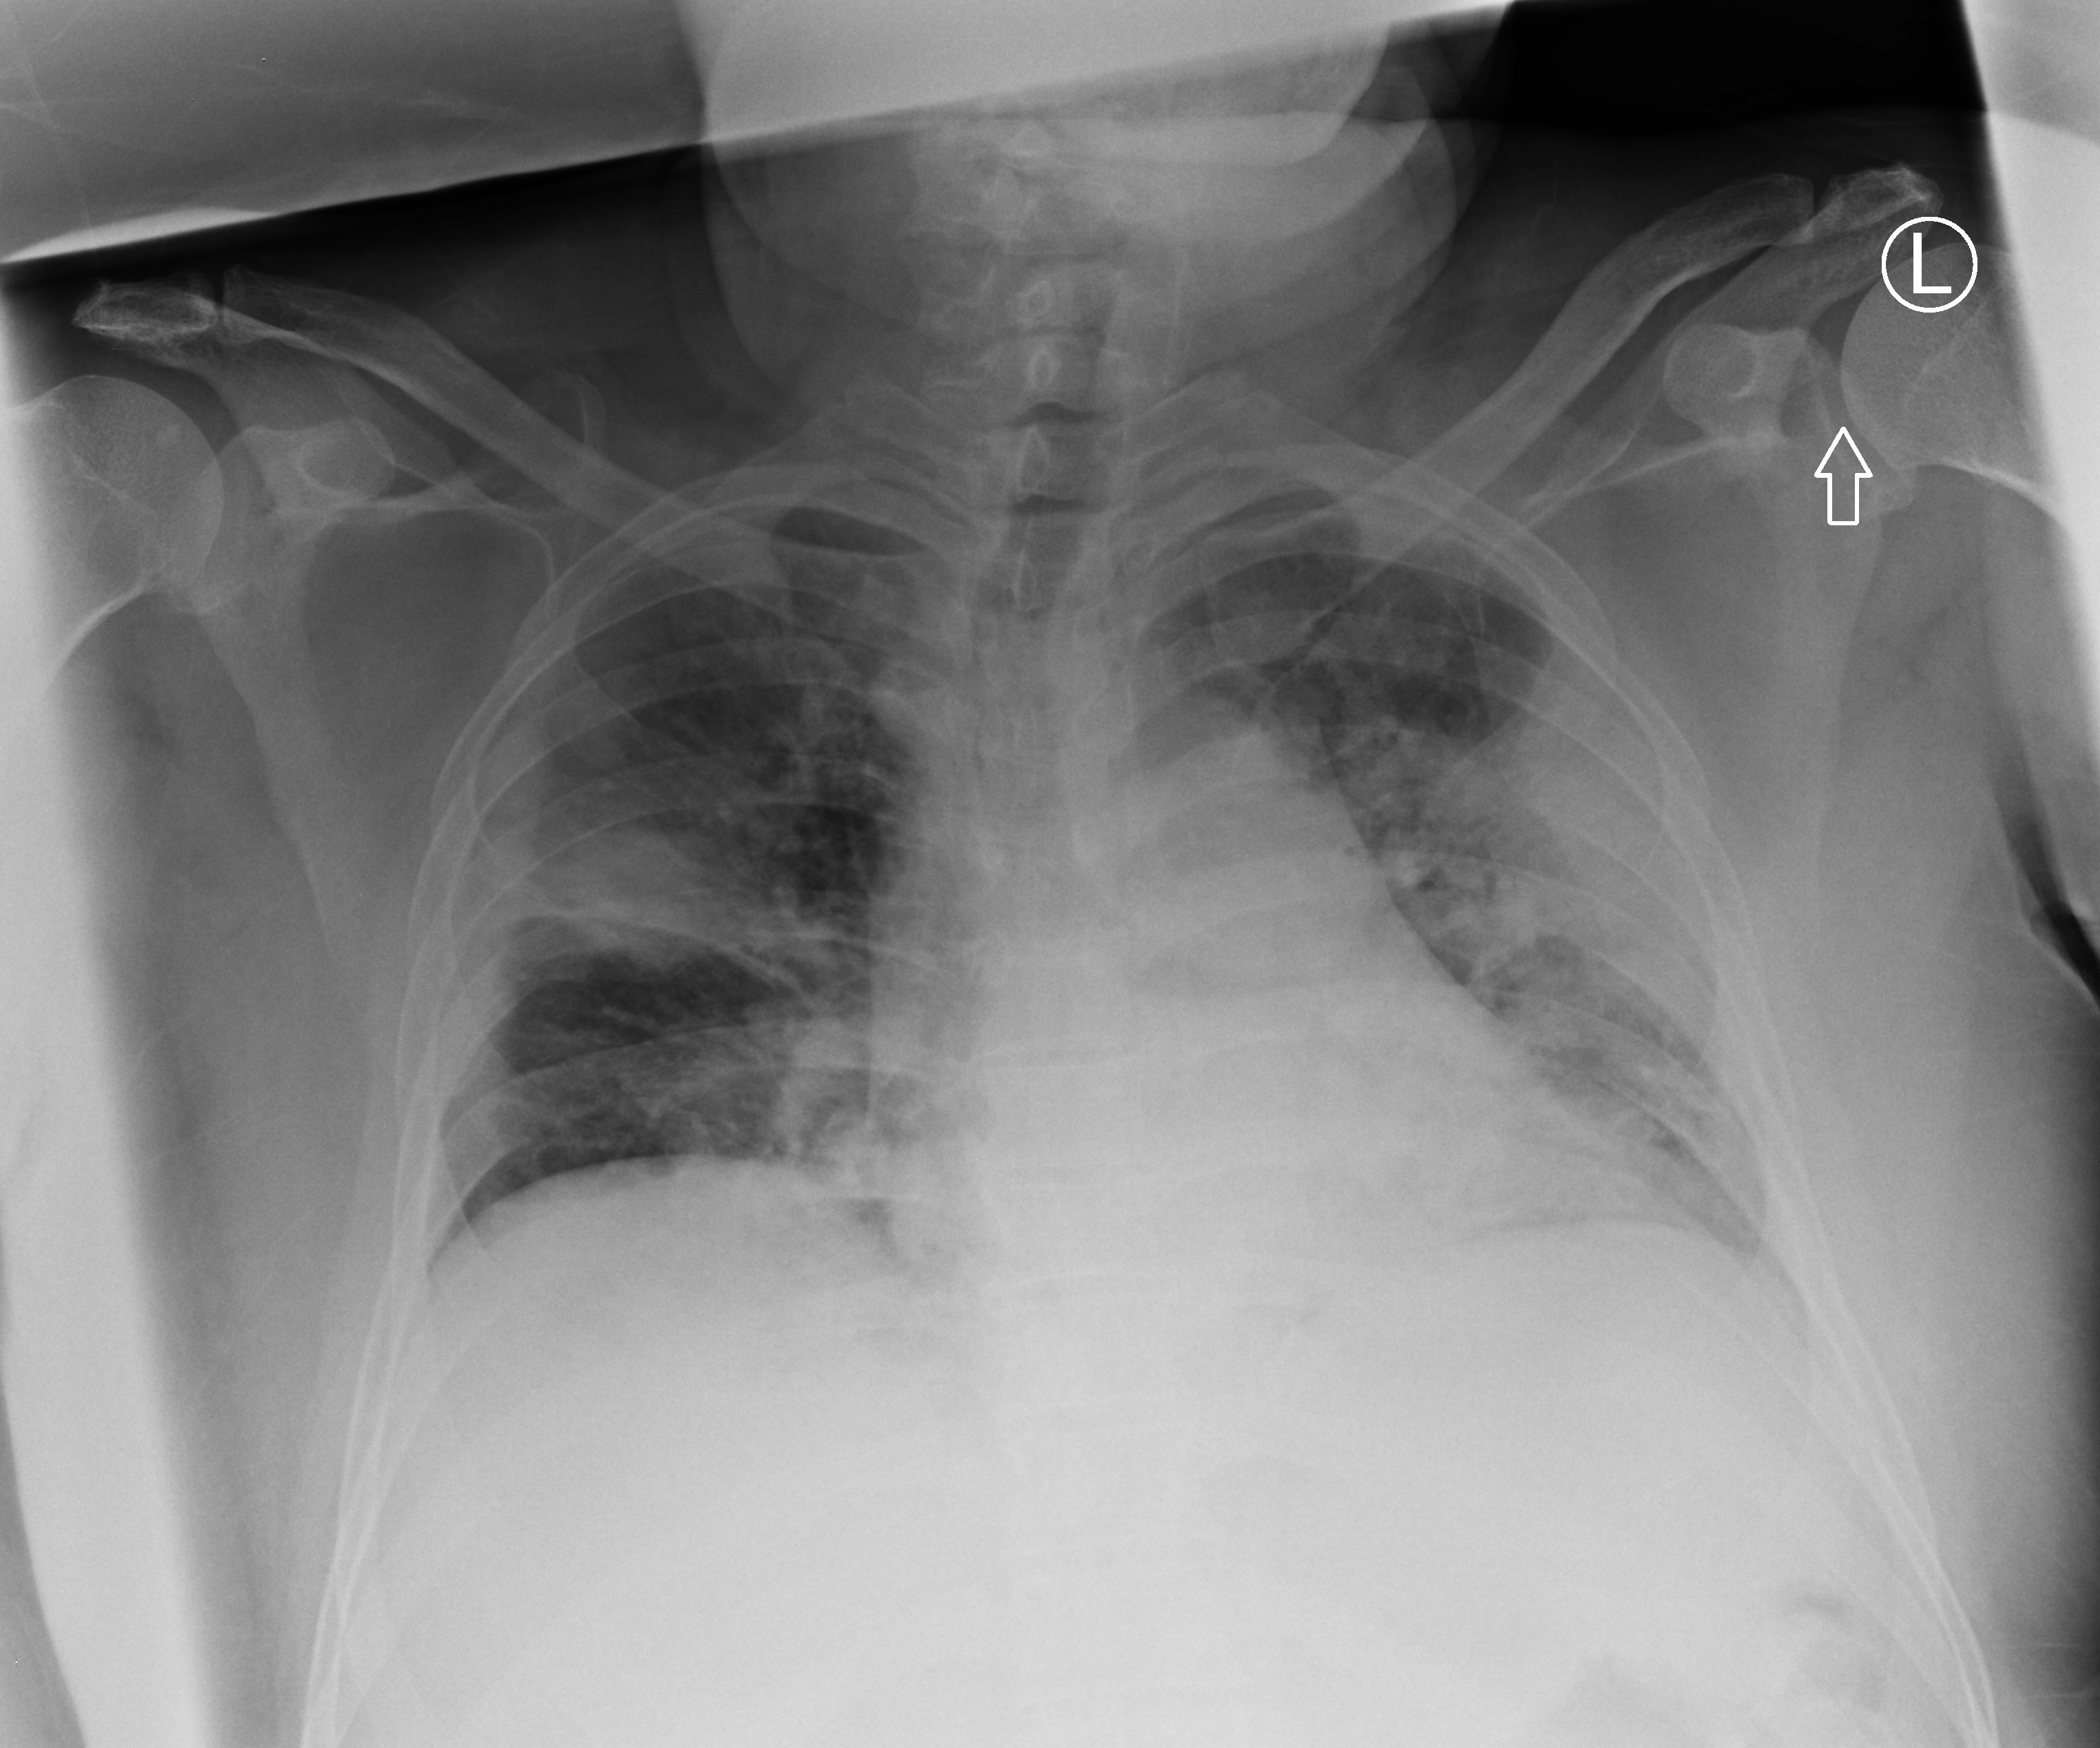
Portable chest radiograph; anteroposterior (AP) projection. Male patient hospitalised with COVID-19, age 18–59 years.
Admission-level facts for this patient (not findings on this image; timing relative to this image not recorded):
- admitted to intensive care during this hospital stay: no
- other chronic lung disease (admission record): no